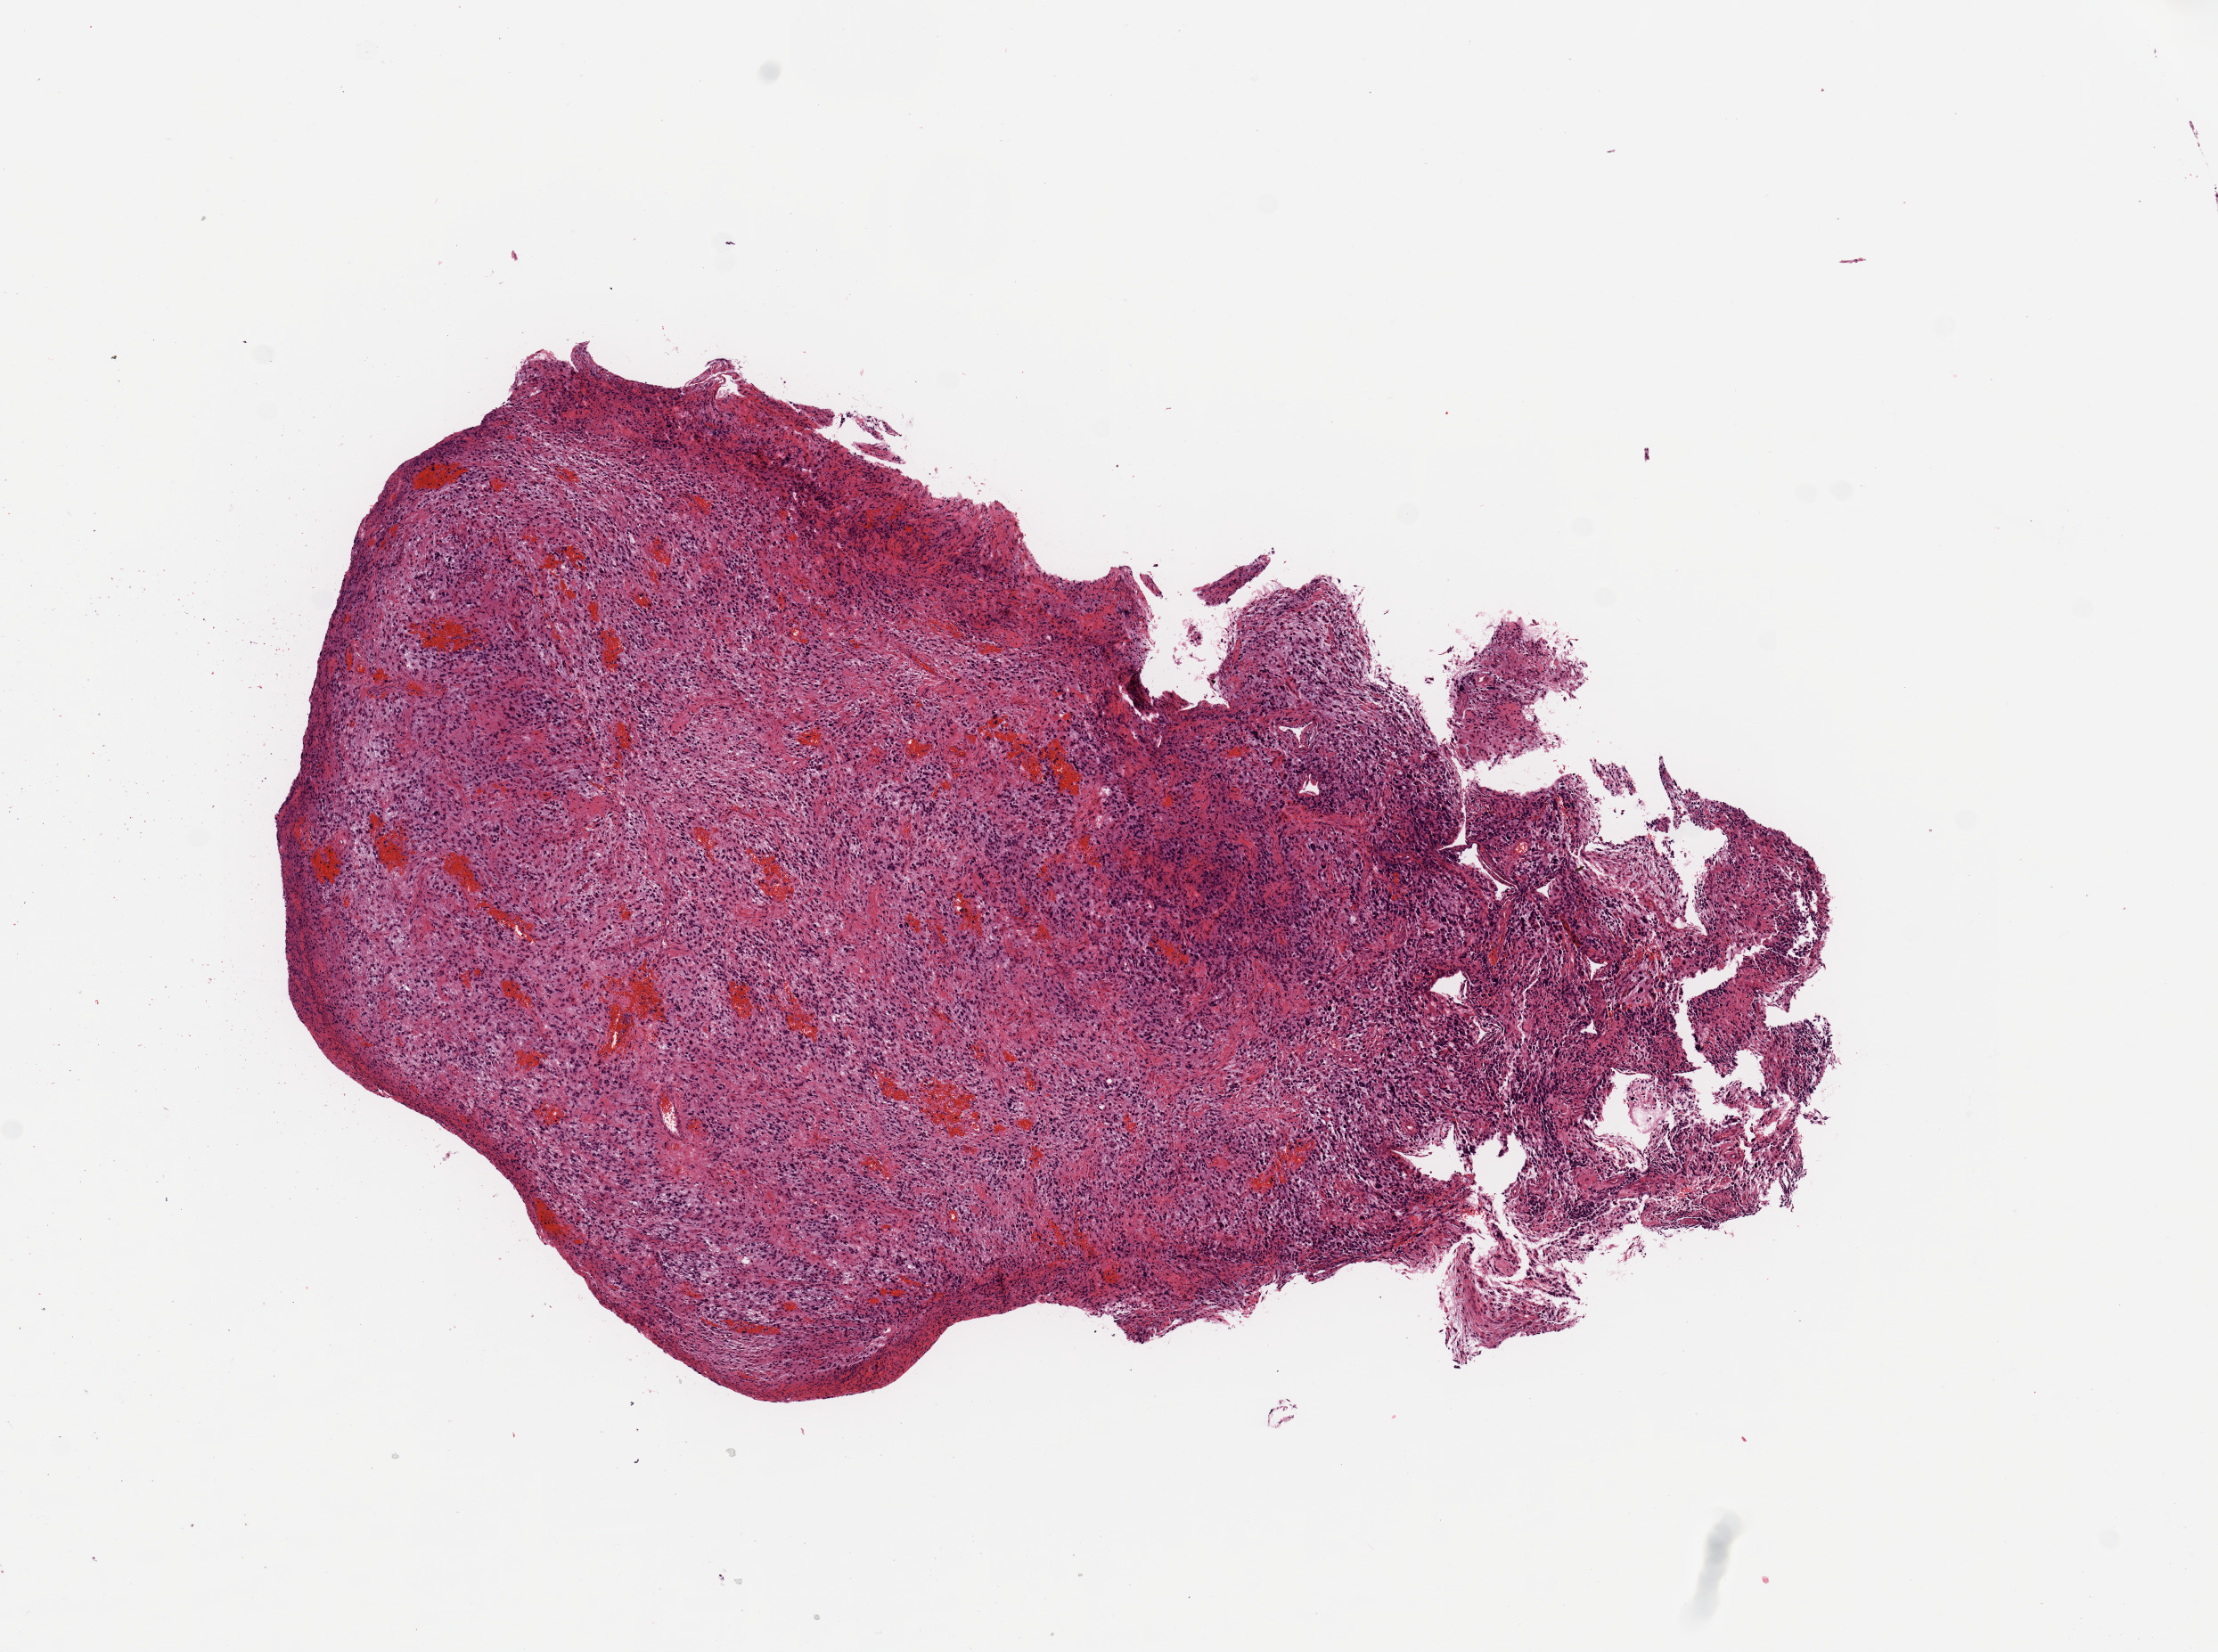
Whole-slide histology image, H&E, shown as a low-resolution overview of the whole scanned area (about 9.8 x 7.3 mm, from a 20x scan); tumour tissue sample, sampled site: brain. Female, 51 y/o. Slide review estimates, as recorded: tumour nuclei 80%, necrosis 5%.
* primary tumour site (as recorded): temporal lobe
* diagnosis: Glioblastoma